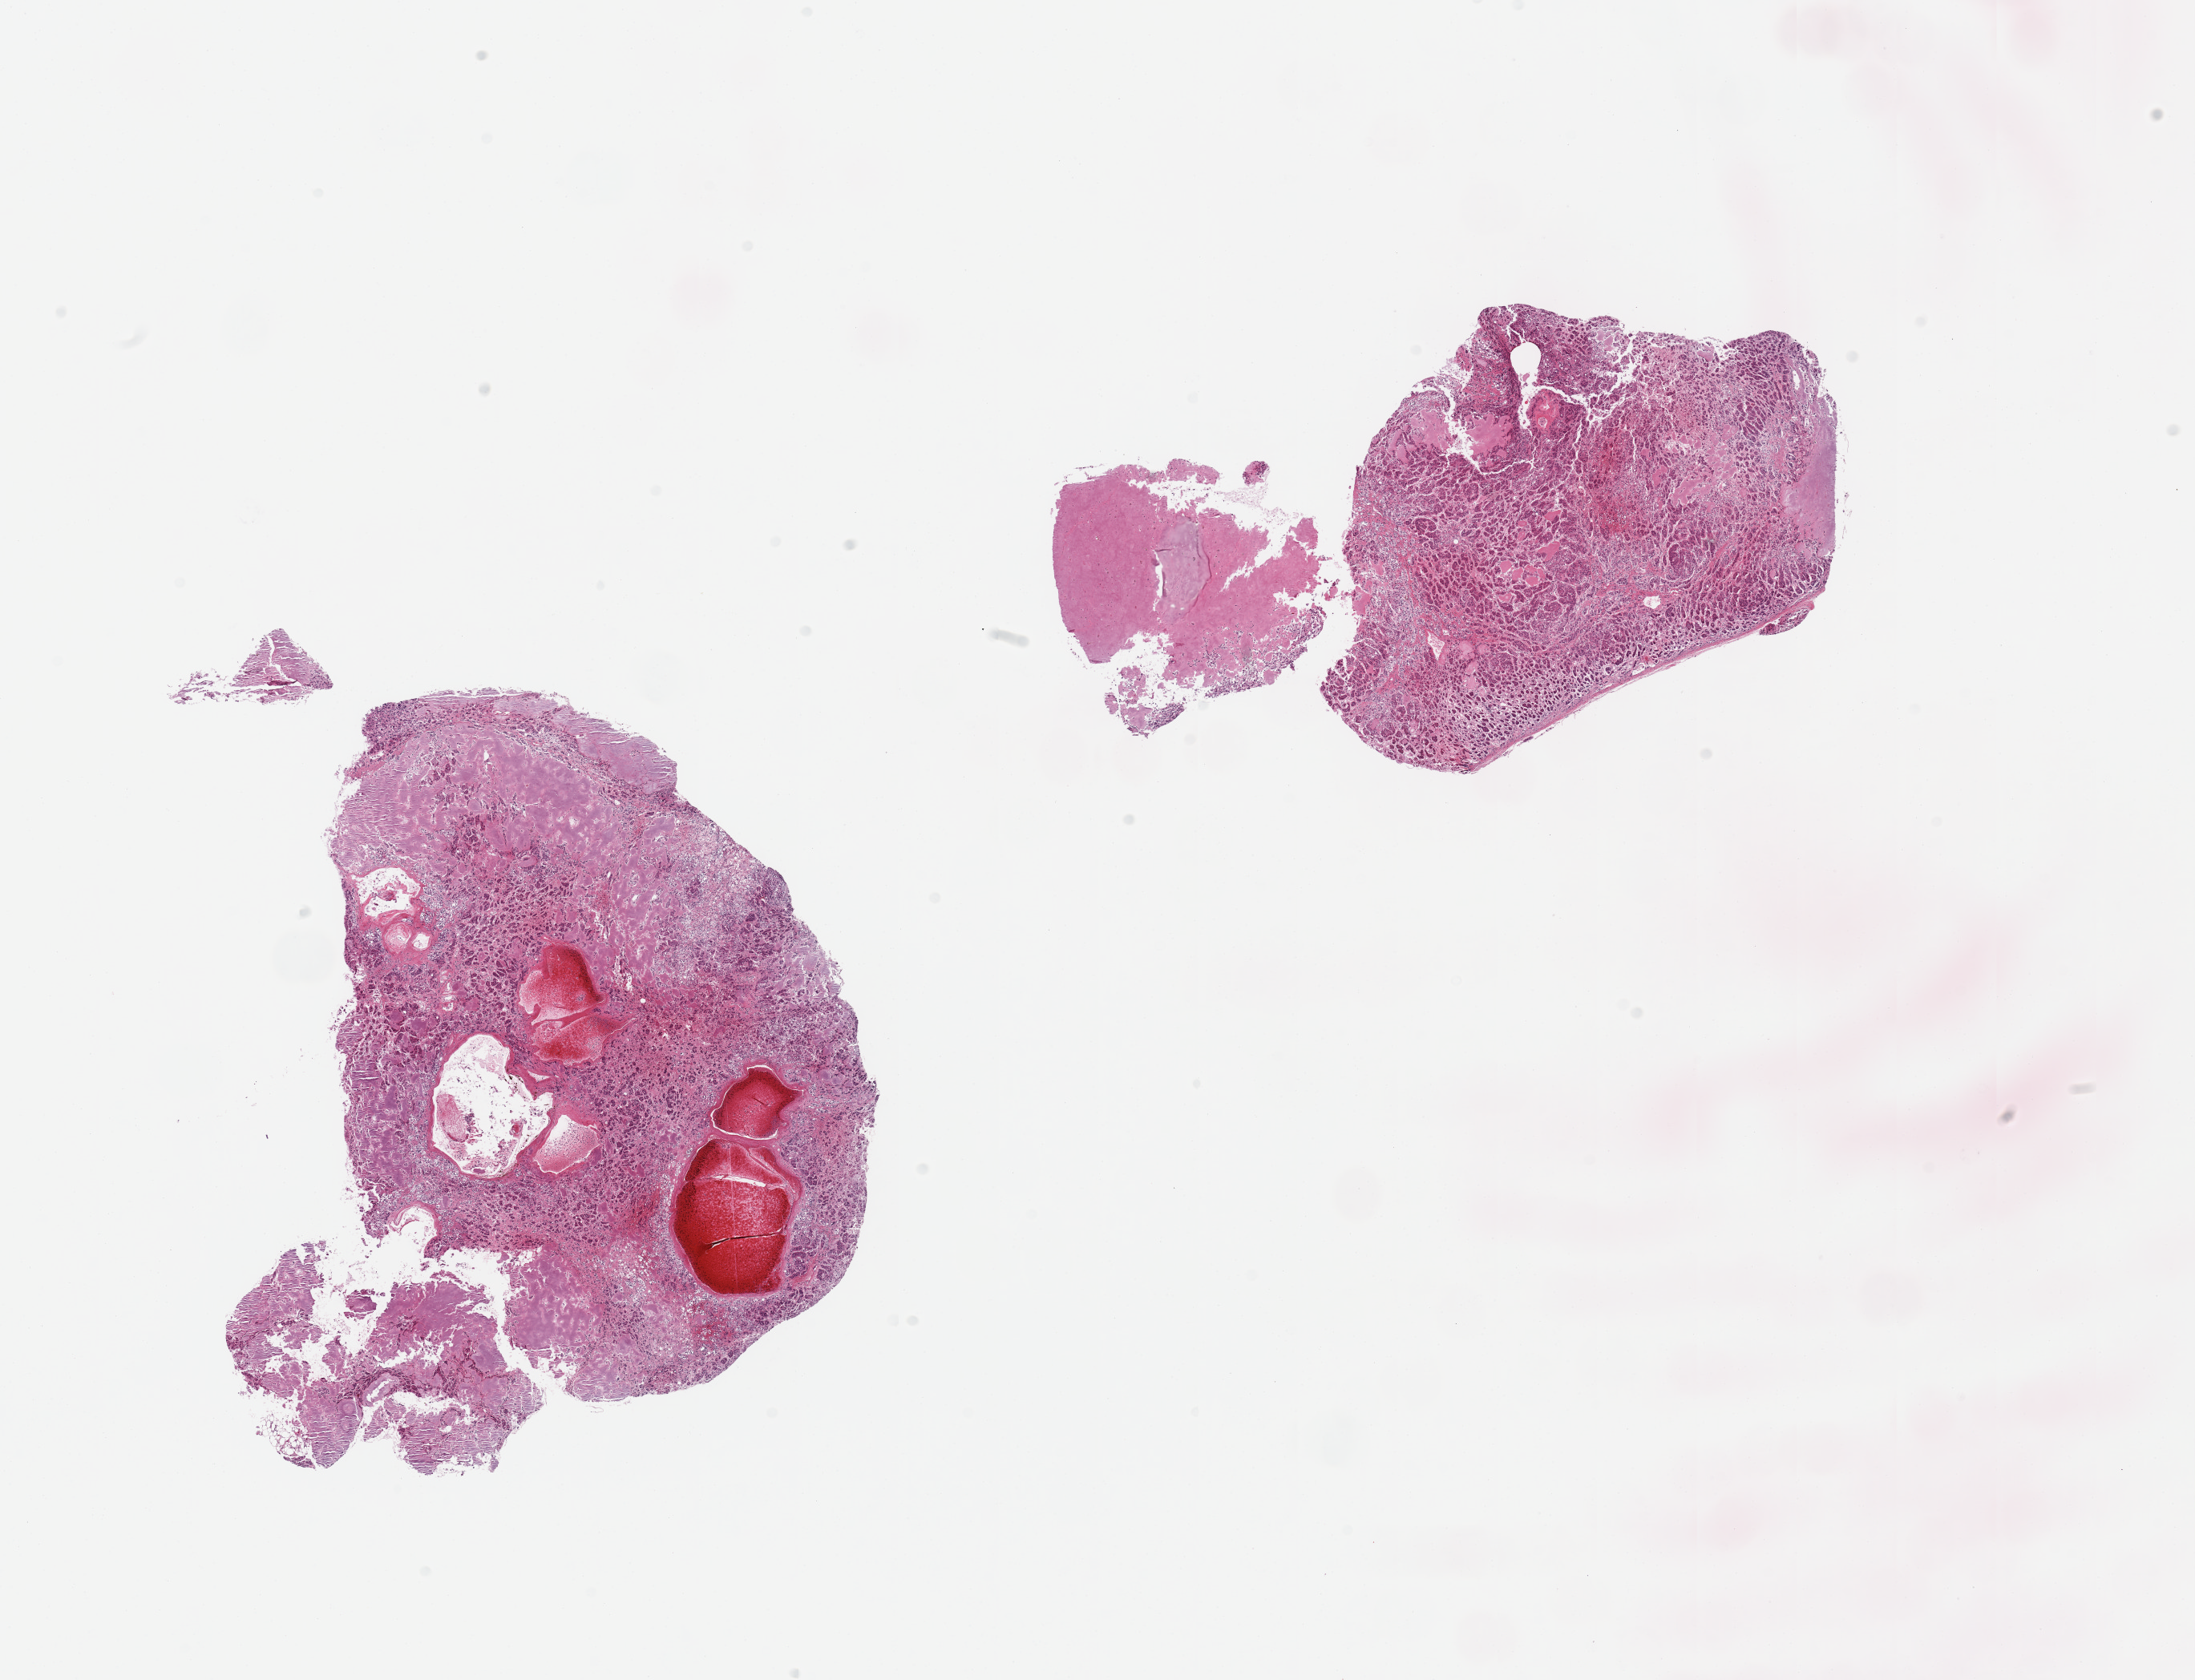
Haematoxylin and eosin whole-slide image, brightfield — shown as a low-resolution overview of the whole scanned area (about 21.7 x 16.6 mm, slide scanned at 20x). PAXgene-fixed paraffin-embedded (PFPE) section. Target tissue: adrenal gland. Tissue donor sample. Donor sex: male.
Pathologist's review note for this sample: 2 pieces, marked autolysis, prominent vessels.